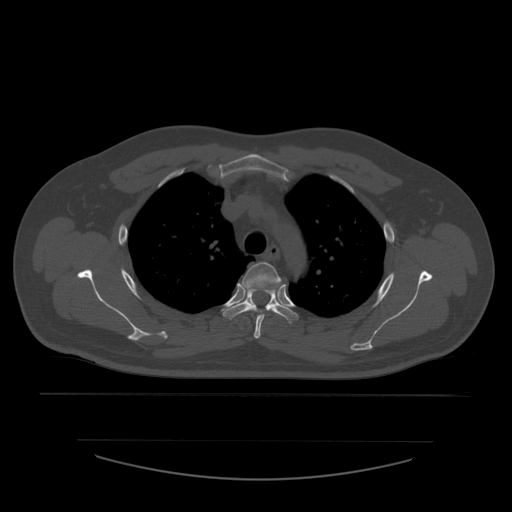
CT including the spine, one axial slice; reconstruction kernel STANDARD; bone window (W 1800 / L 400 HU); 512 × 512 image matrix, field of view 441 × 441 mm. Patient age 44 years. From the clinical record (not read from this slice): primary cancer: soft tissue sarcoma.
Structures marked on this image (semi-automatic segmentation, software-assisted and operator-edited):
- T3 vertebra: box from (x=241, y=262) to (x=283, y=339) px
- T4 vertebra: (x=223, y=290)–(x=298, y=324)